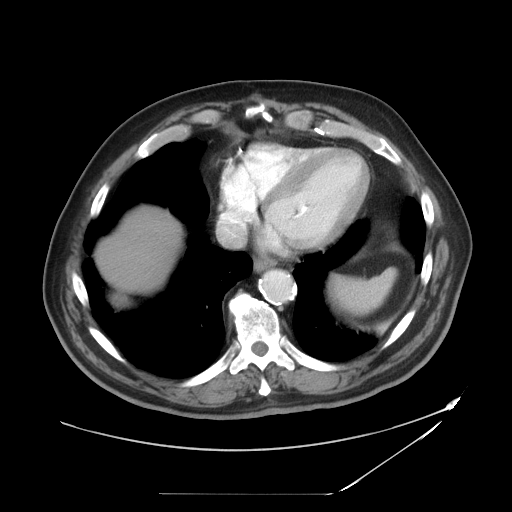
Contrast-enhanced abdominal CT, one axial slice. Position 42 of 49 along the scan axis. 120 kVp. Soft-tissue window (W 400 / L 40 HU). 5 mm slice thickness. 512 × 512 image matrix, field of view 461 × 461 mm. Male patient, age 72 years. From the clinical record (not read from this slice): diagnosis: colorectal cancer liver metastases, imaged before liver resection; multiple liver metastases: no.
Structures marked on this image (outlined manually by an expert reader):
- liver: box from (x=100, y=210) to (x=177, y=294) px
- planned liver remnant (the part of the liver to remain after resection): (x=100, y=210)–(x=178, y=294)